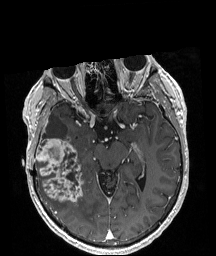
Brain MRI from a brain-tumour surgery series, one axial slice; T1-weighted post-contrast; 1 mm slice thickness; 216 × 256 image matrix, field of view 211 × 250 mm. Case-level facts recorded for this patient, not image findings: histopathology: Astrocytoma; WHO grade: 4; IDH mutation: yes; tumour location: Right Temporal.
Annotated regions visible in this slice (outlined manually by an expert reader):
- tumour: box from (x=36, y=136) to (x=83, y=202) px